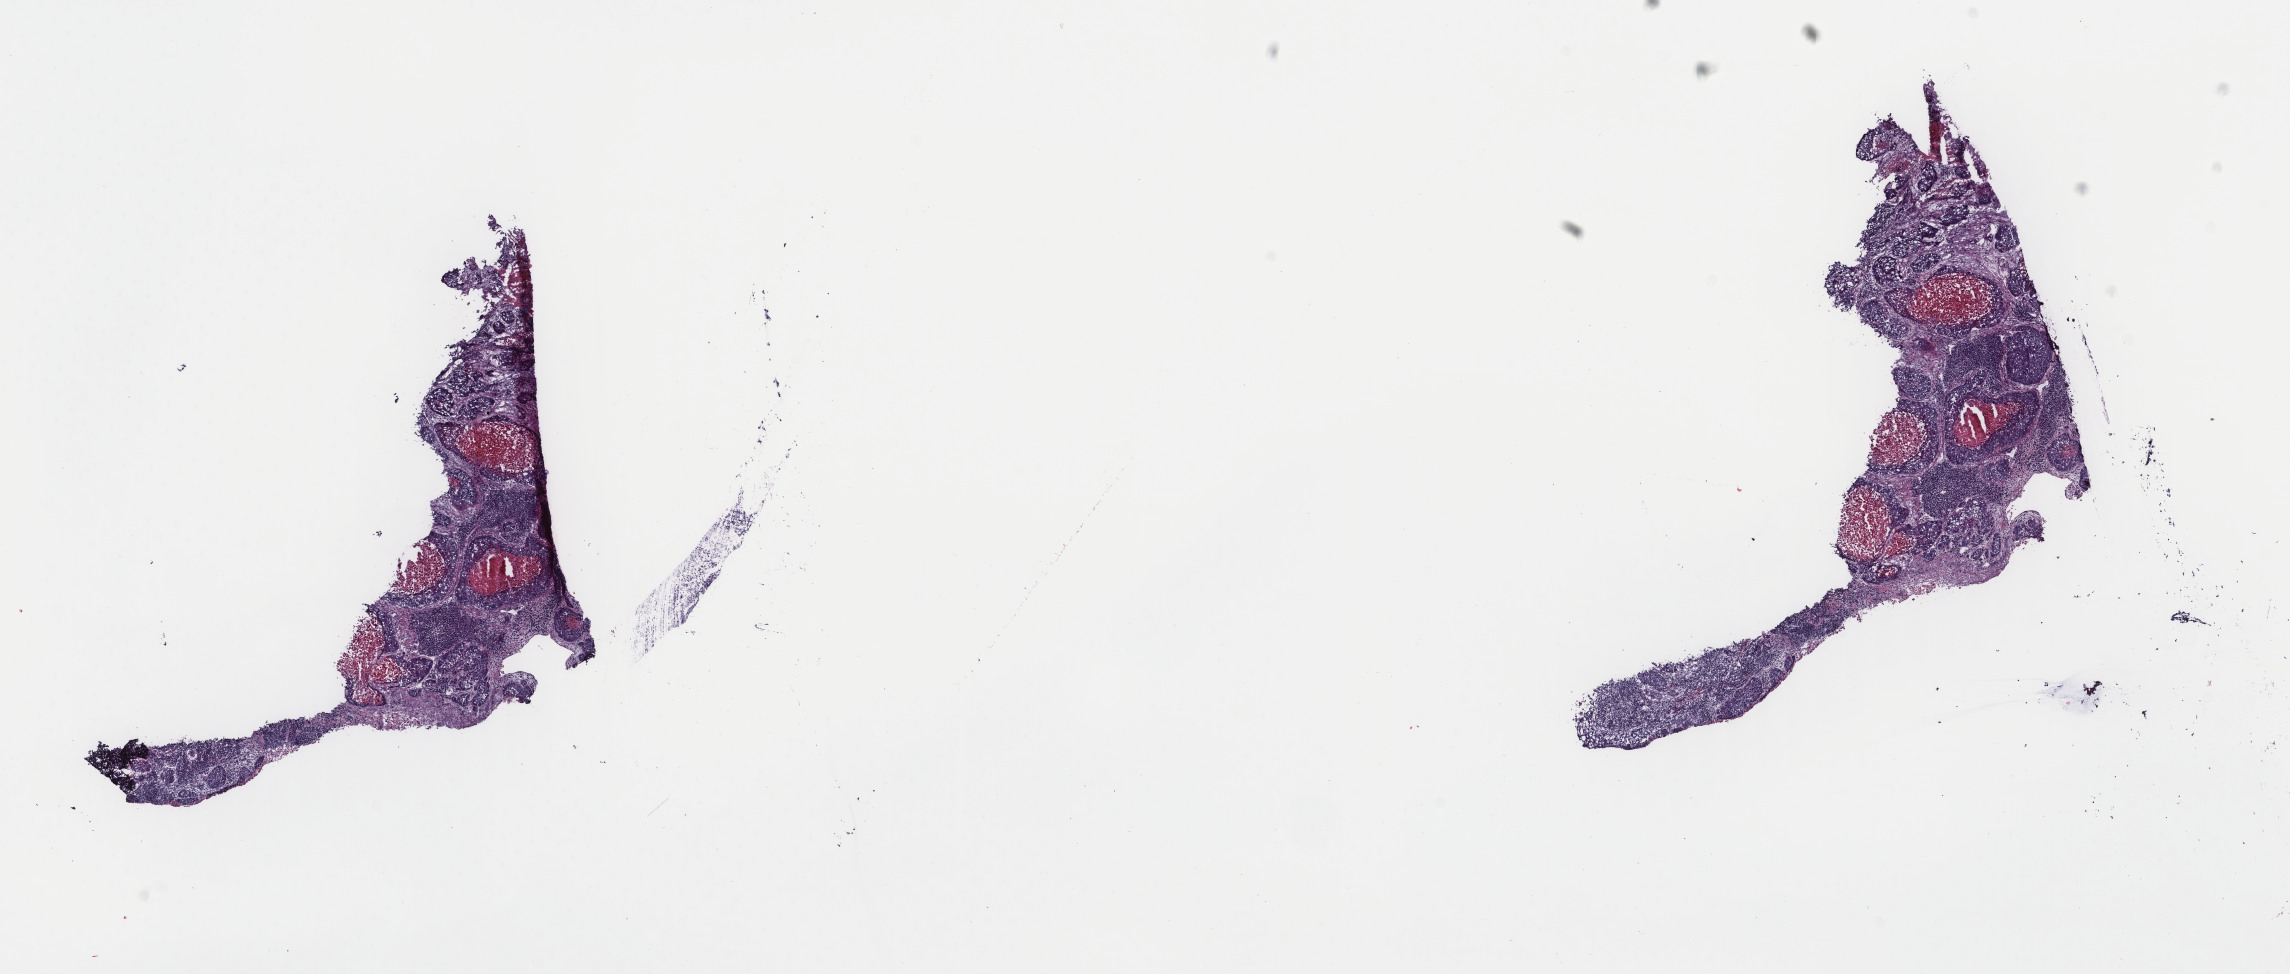
Digitized H&E-stained tissue section (whole slide), a low-resolution overview of the entire scanned area, about 18.2 x 7.7 mm (slide scanned at 40x), frozen section, lung, primary tumour sample. Patient: male, age at initial diagnosis 70 years. Slide review estimates, as recorded: tumour cells 65%, tumour nuclei 65%, normal cells 0%, stromal cells 20%, necrosis 15%. Infiltration values recorded for this section: lymphocyte infiltration 6%, monocyte infiltration 2%, neutrophil infiltration 4%.
AJCC pathologic stage: IIA (7th edition). Pathologic diagnosis: Squamous cell carcinoma, NOS (lower lobe, lung).